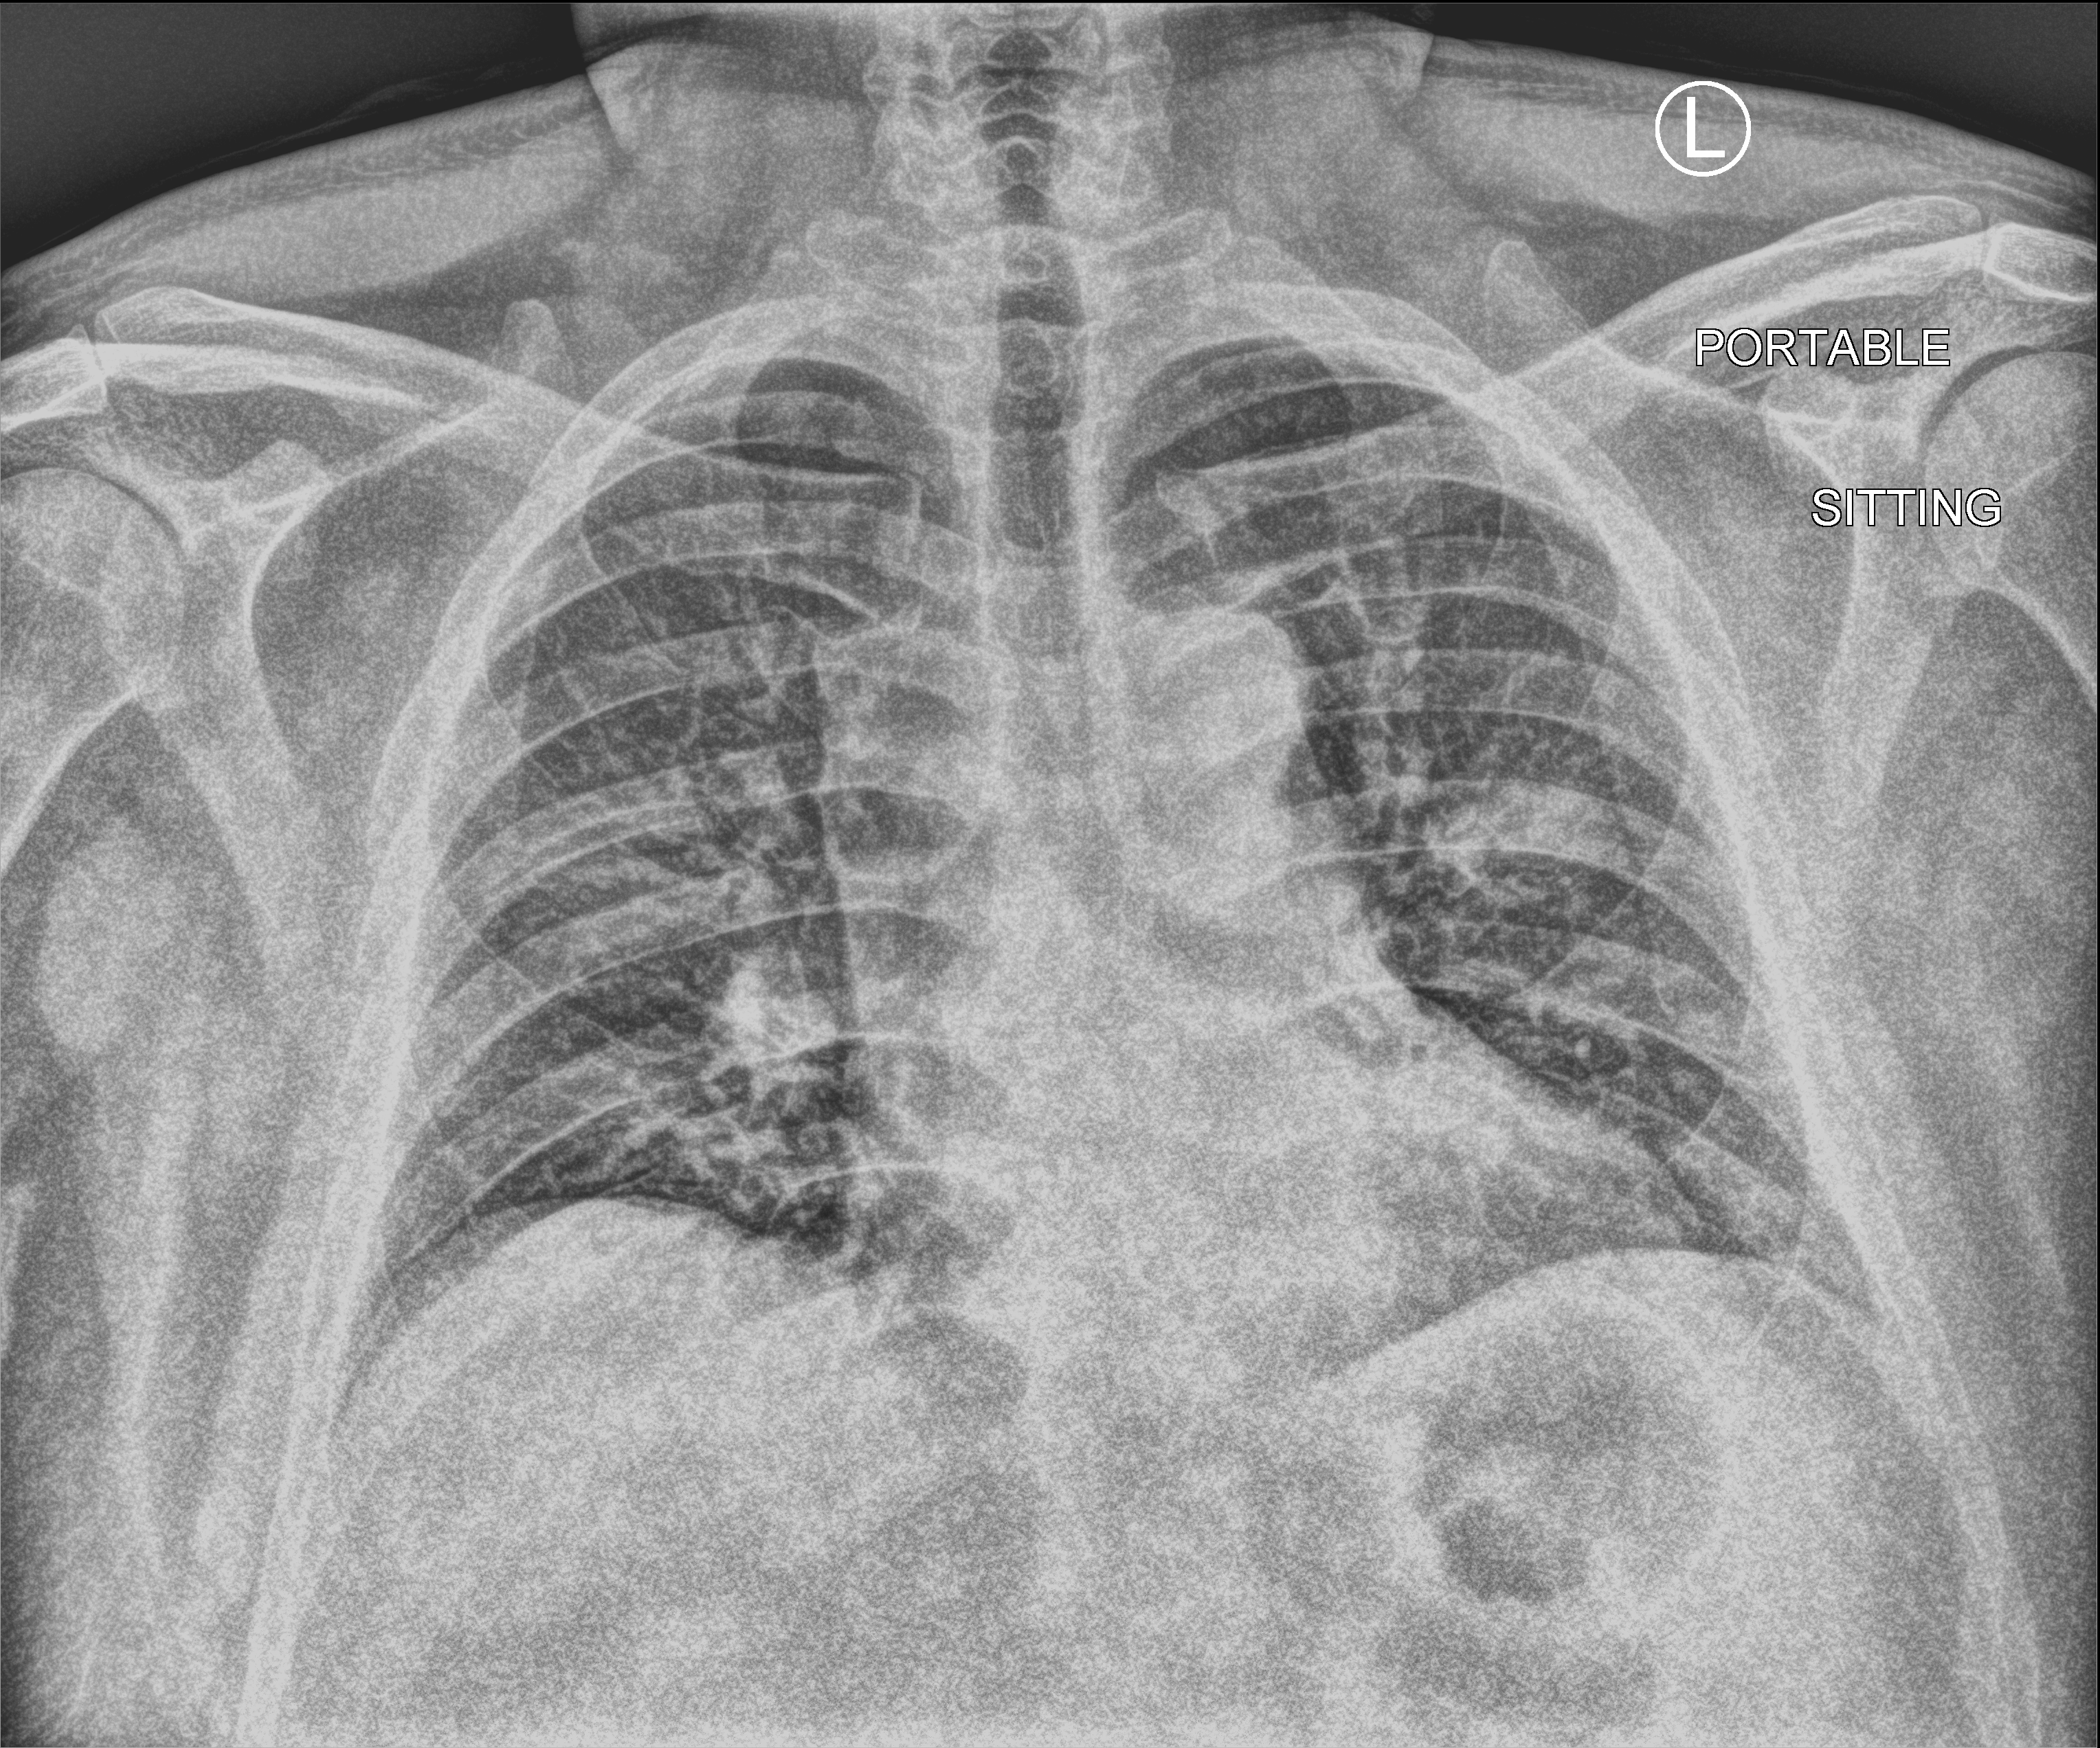
Portable chest radiograph, anteroposterior (AP) projection. Patient hospitalised with COVID-19; male, aged 18–59 years.
From the hospital-stay record, not from the radiograph (when in the stay this image was taken is not recorded):
- admitted to intensive care during this hospital stay: no